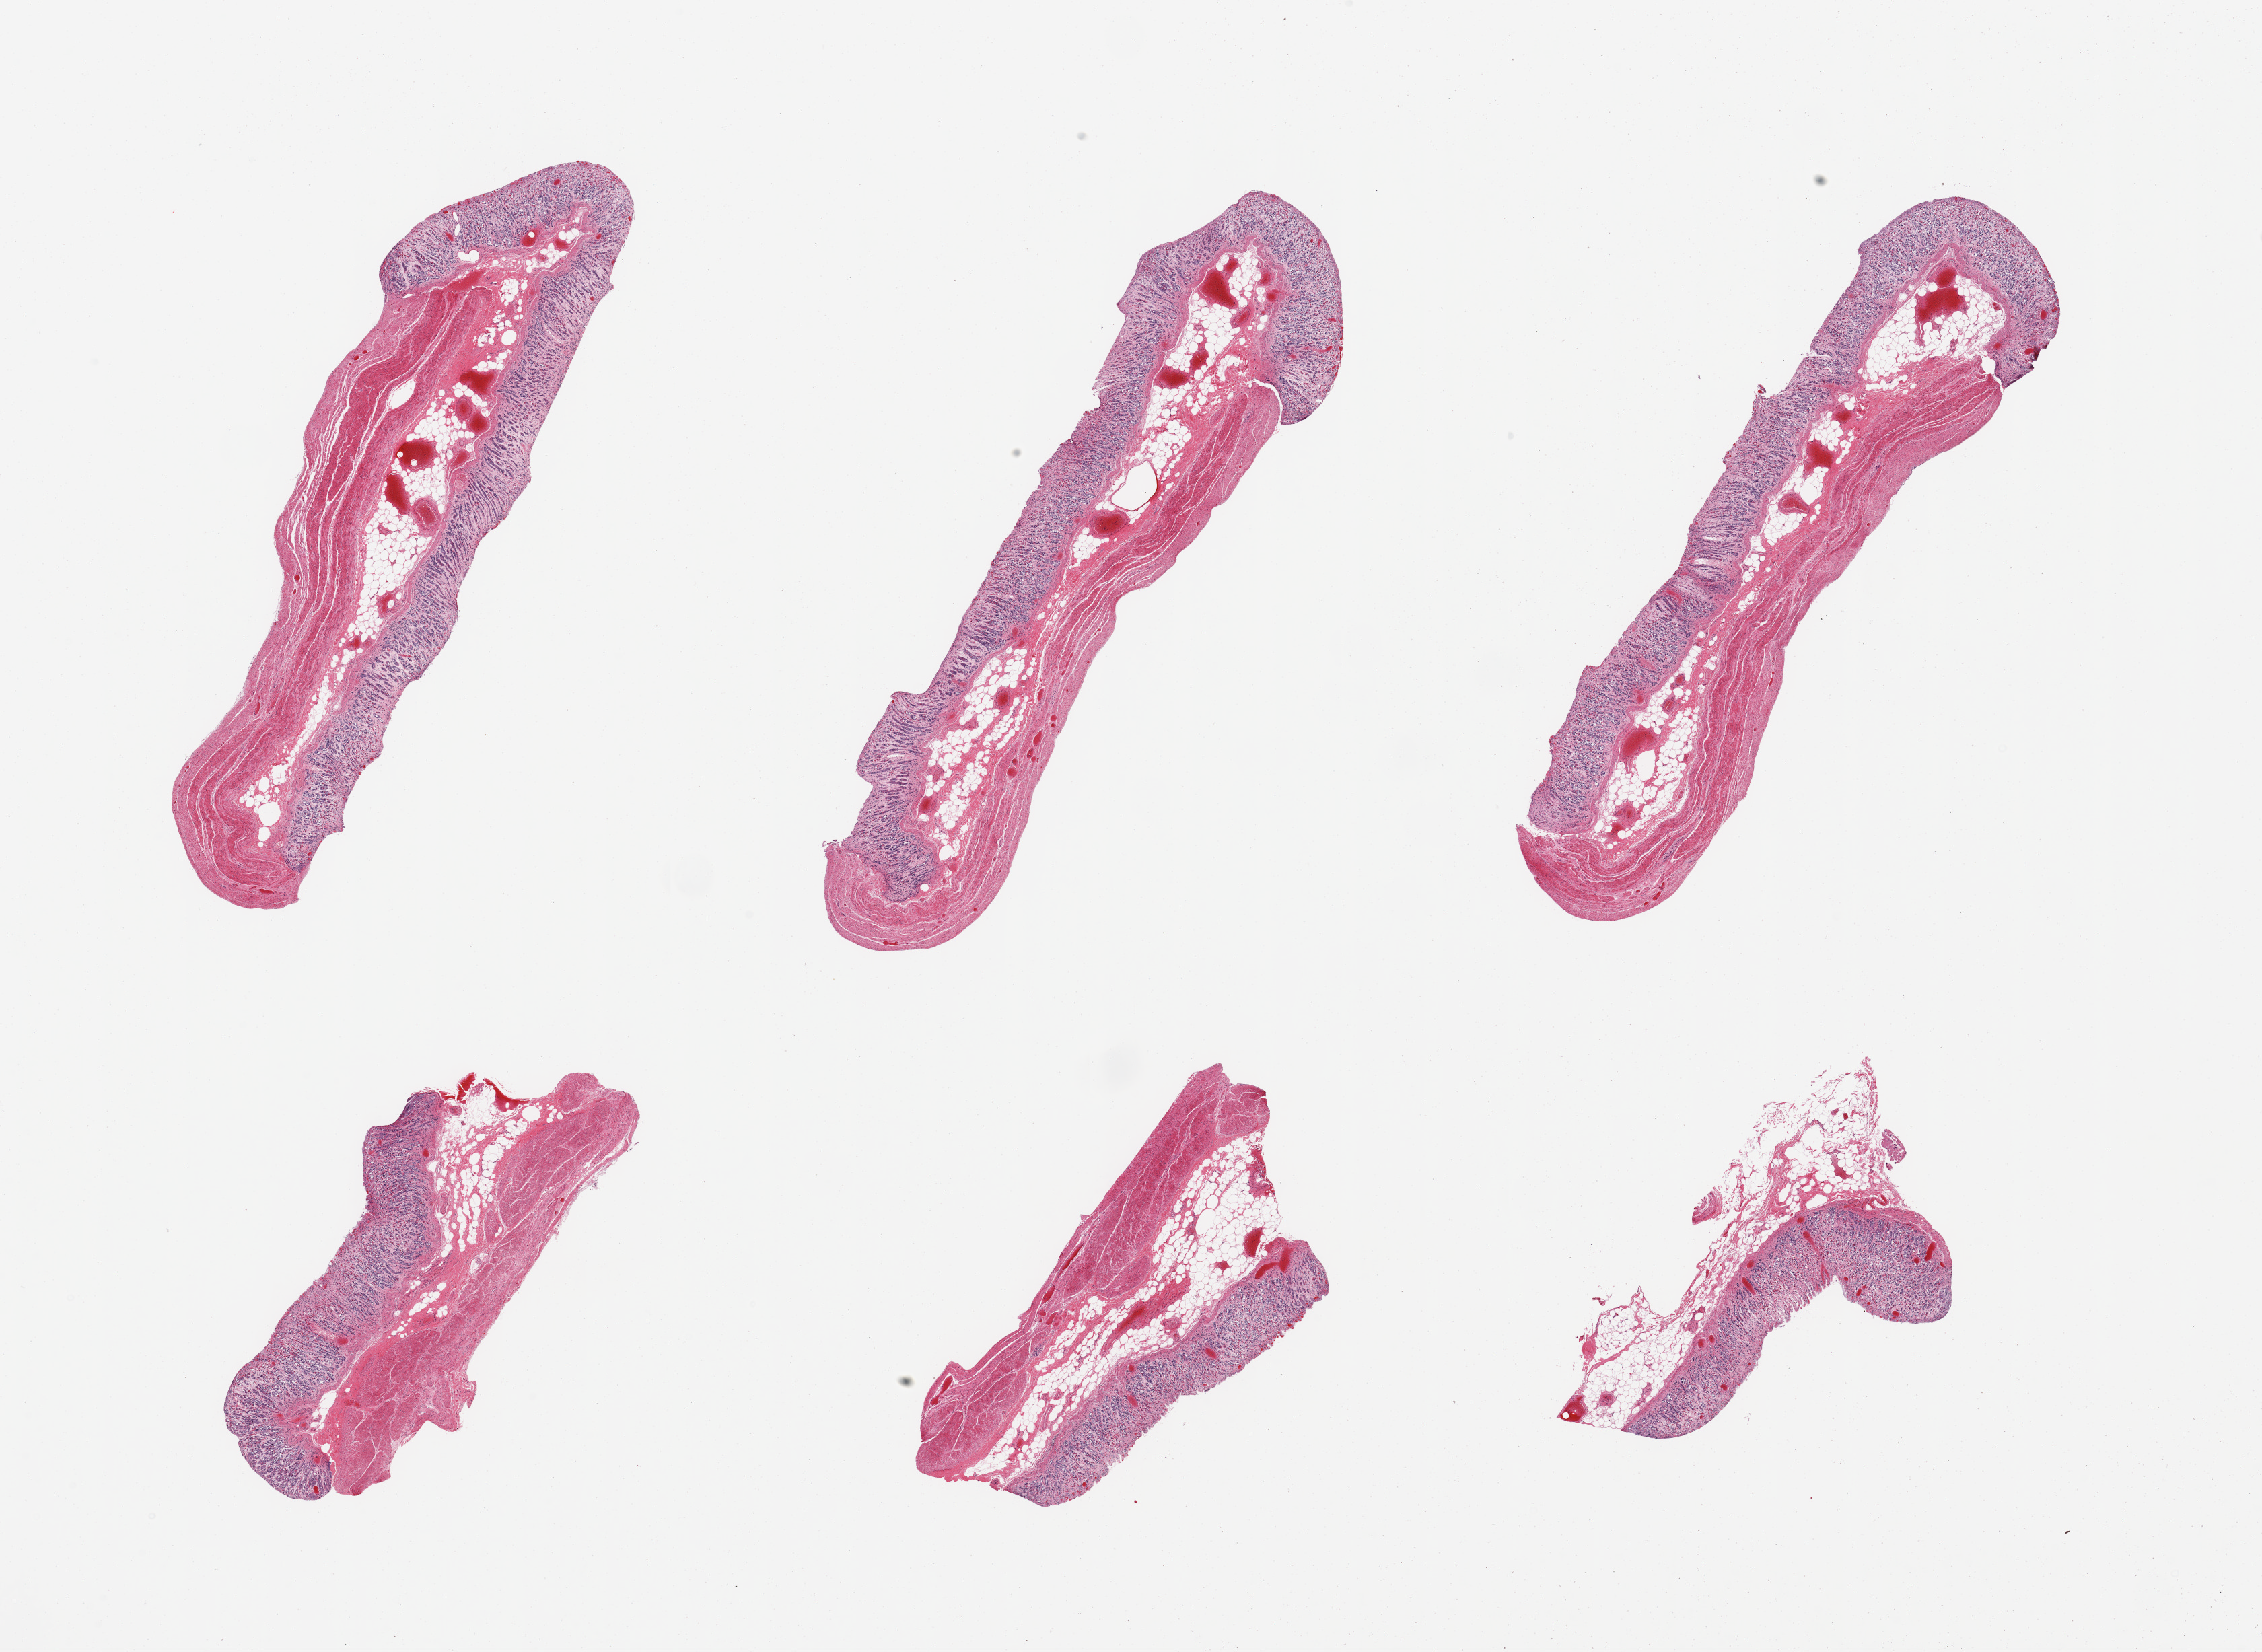
Whole-slide image, haematoxylin and eosin stain — whole scanned area (about 26.6 x 19.4 mm) shown as a low-resolution overview; PAXgene-fixed, paraffin-embedded tissue; sampled site (target tissue): stomach; donor tissue sample.
* reviewer comment on this tissue sample: 6 pieces, glandular mucosa with moderately advanced autolysis, up to ~0.6mm, ~30% of thickness